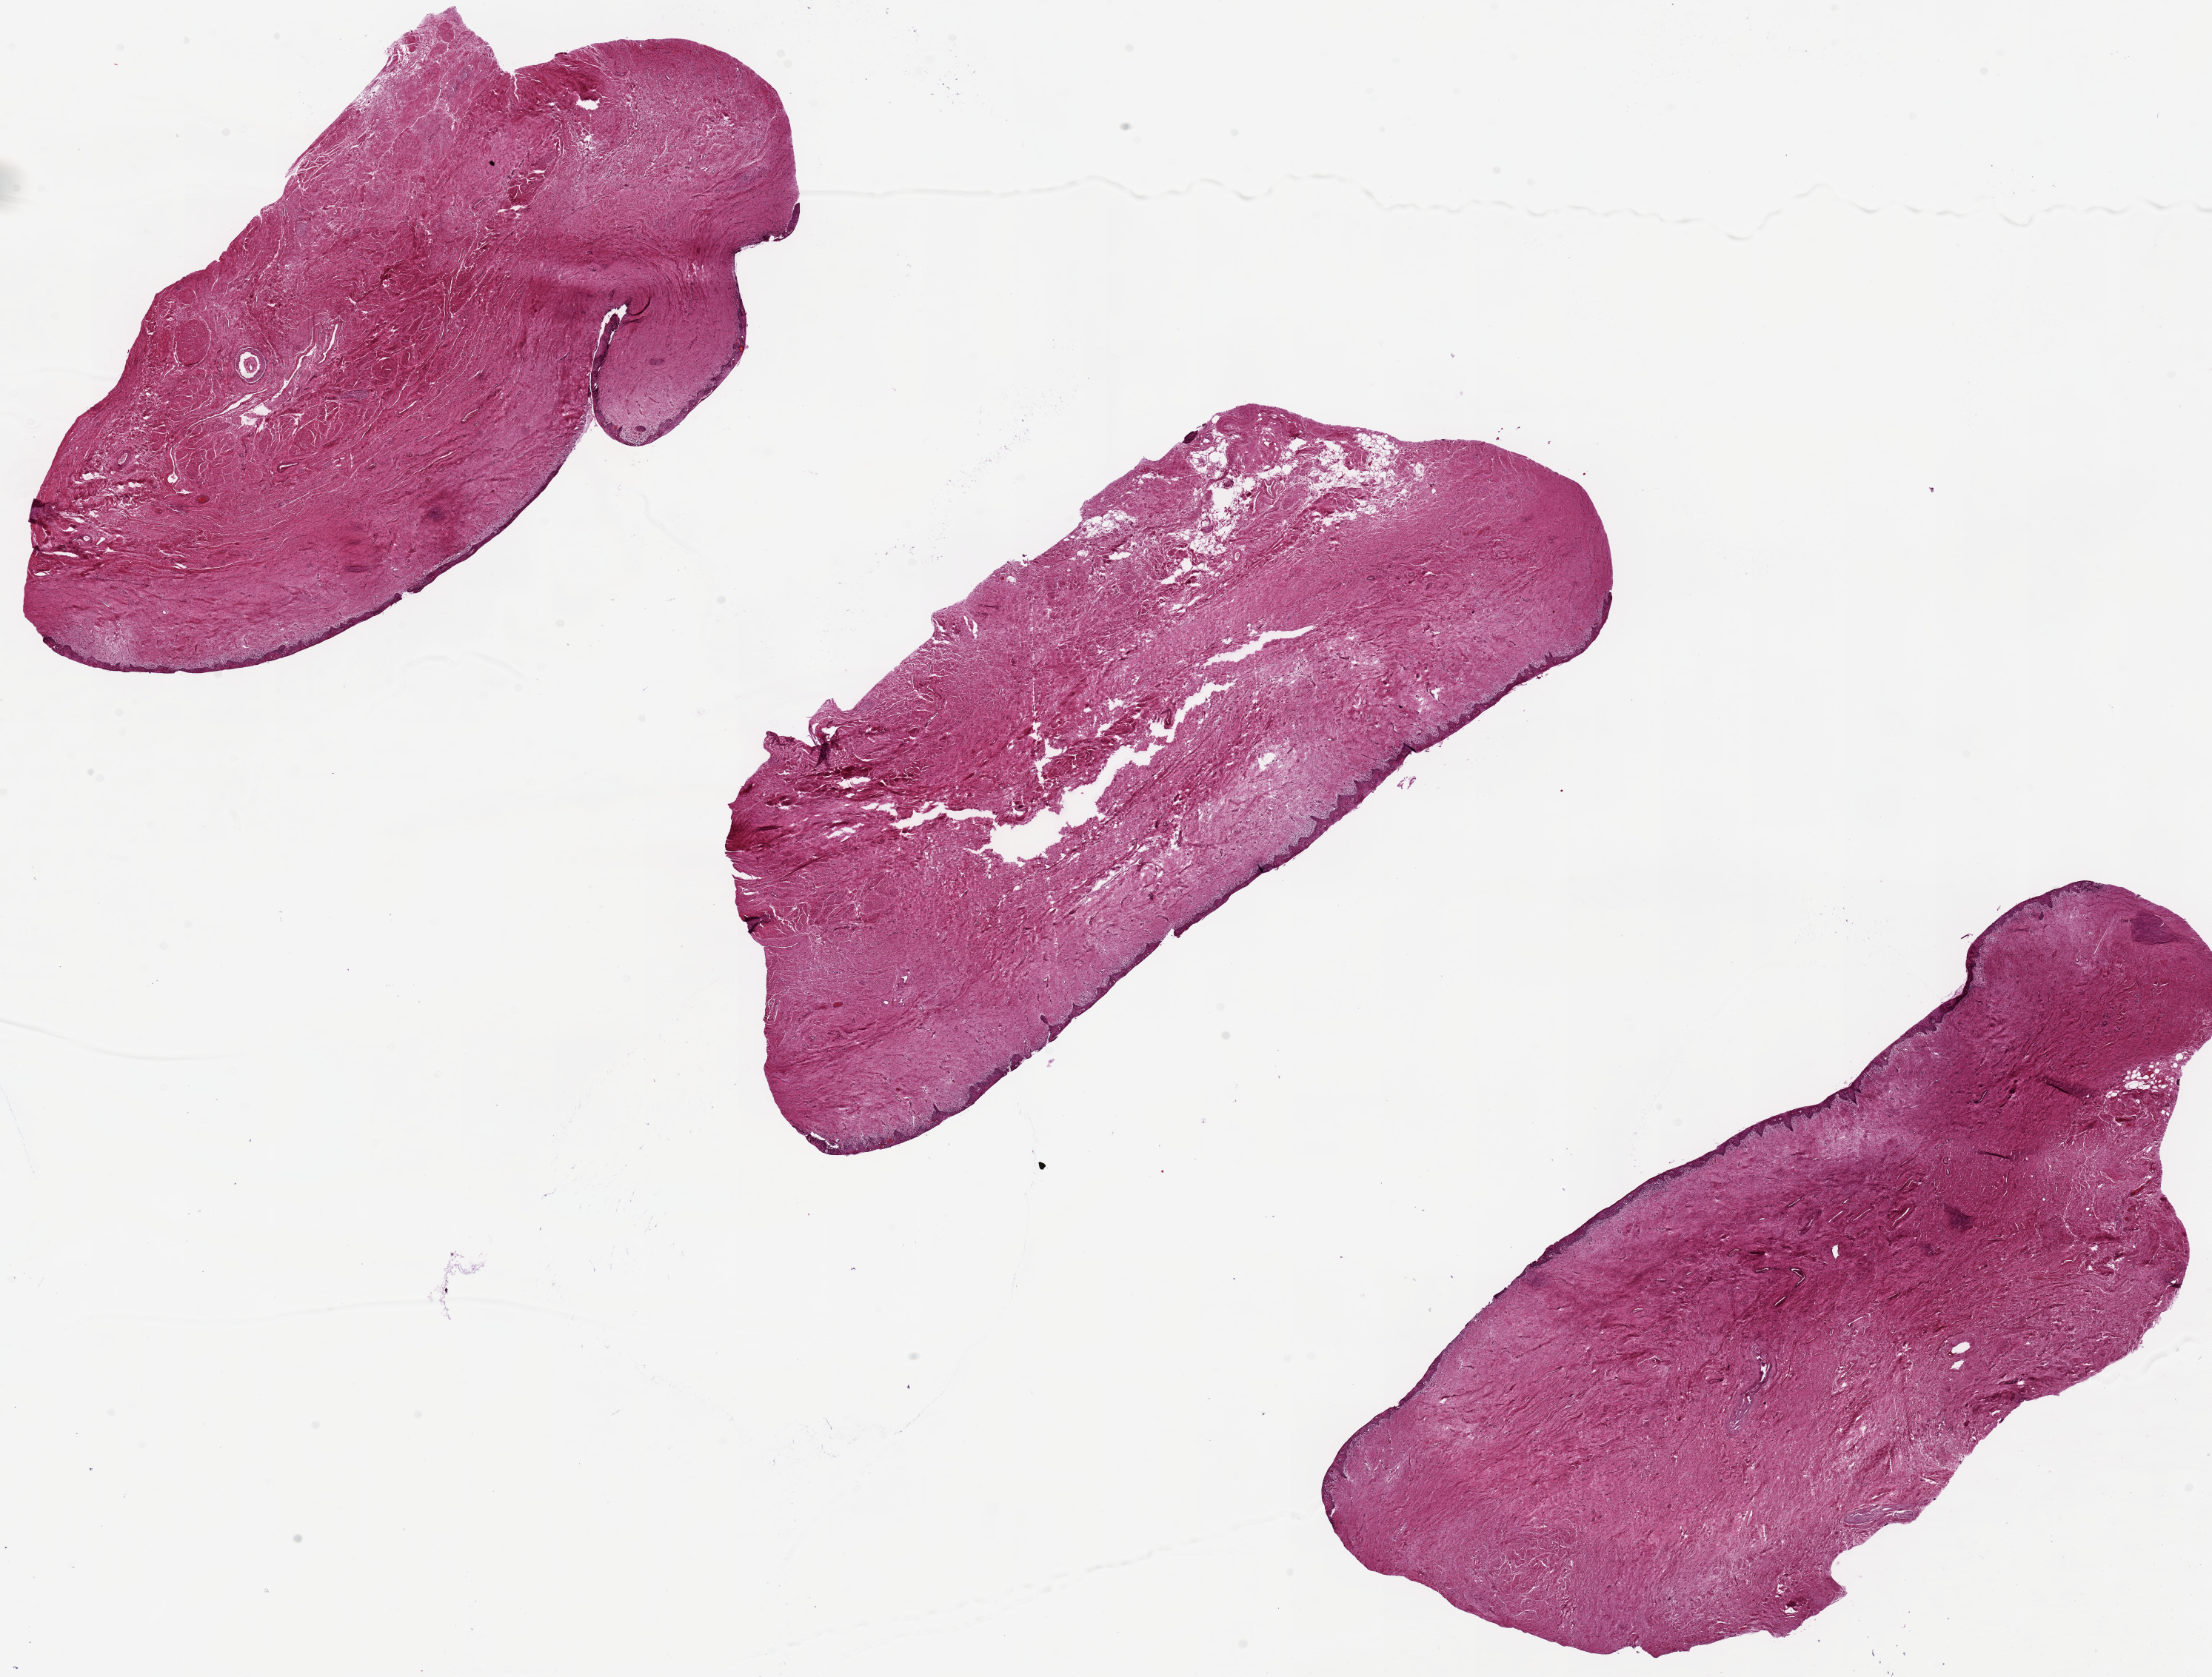
H&E whole-slide image, shown as a low-resolution overview of the whole scanned area (about 23.6 x 17.9 mm, slide scanned at 20x). PAXgene-fixed, paraffin-embedded tissue. Section of vagina (target tissue). Tissue donor sample. Donor: female.
* pathologist's review note for this sample: Squamous mucosa is 1% total thickness of specimen